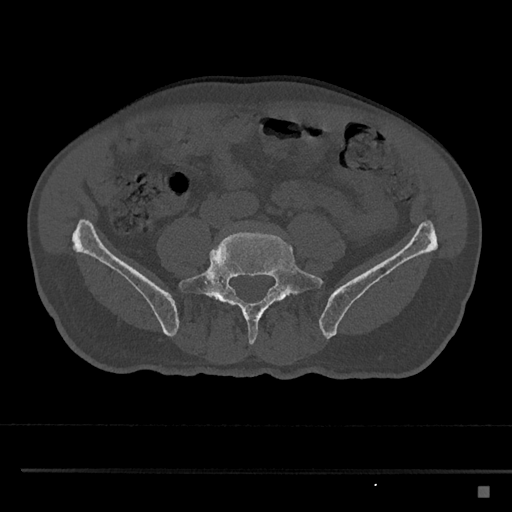
CT including the spine, one axial slice; position 587 of 797 along the scan axis; reconstruction kernel Br40s/3; bone window (W 1800 / L 400 HU); 512 × 512 image matrix, field of view 391 × 391 mm. Patient: male, 59 years. From the clinical record (not read from this slice): primary cancer: prostate.
Structures marked on this image (semi-automatic segmentation, software-assisted and operator-edited):
- L5 vertebra: bounding box (x1, y1, x2, y2) in pixels: (179, 230, 323, 345)